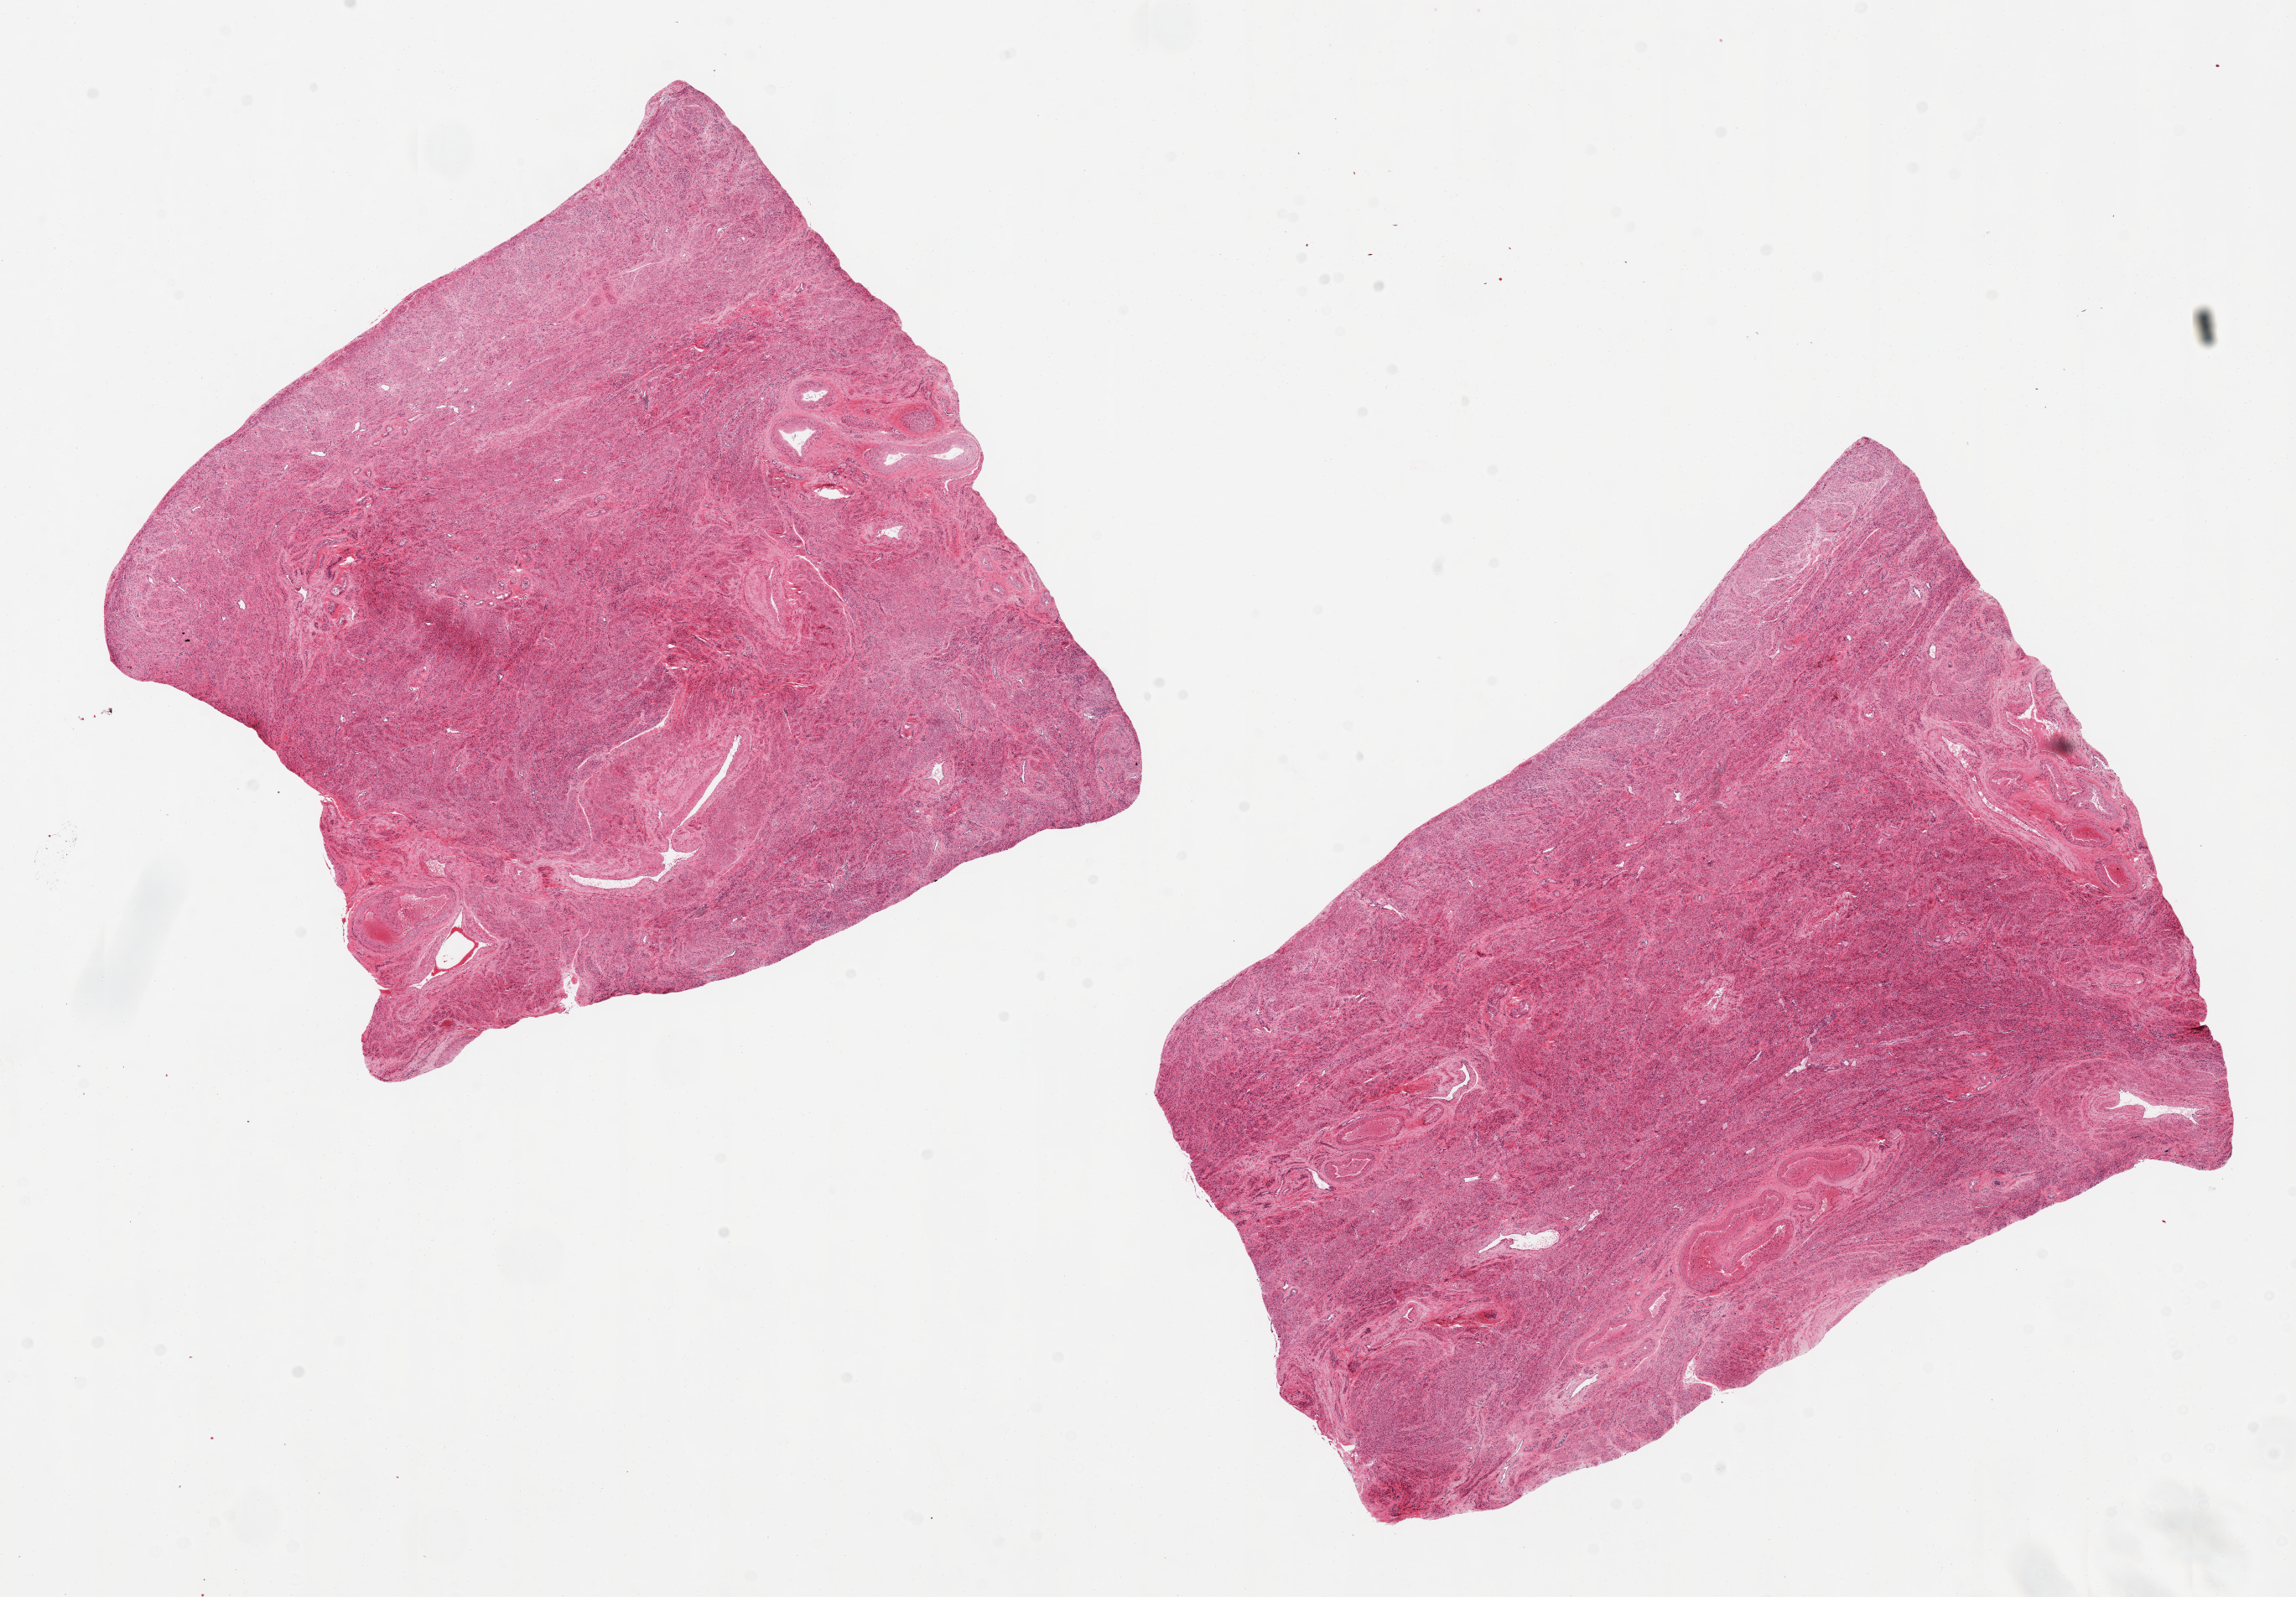
Digitized hematoxylin and eosin (H&E)-stained section — low-resolution overview of the scanned area, about 21.7 x 15.1 mm (acquisition: 20x scan); PAXgene-fixed, paraffin-embedded tissue; target tissue: uterus; tissue donor sample. Donor: female.
Reviewer comment on this tissue sample: 2 pieces, all myometrium, no visible endometrial glandular/stromal elements.